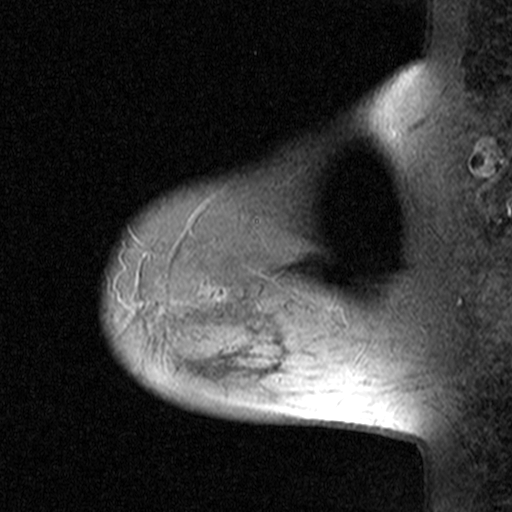
Breast MRI (dynamic contrast-enhanced), one sagittal slice; position 36 of 44 along the scan axis; dynamic contrast-enhanced study with each time point stored as its own series, time point 2 of 3 at this slice position (early post-contrast, ordered by acquisition time); 1.5 T; TE 4.5 ms, TR 11 ms; 512 × 512 image matrix. Patient: female, 38 years. Case-level facts recorded for this patient, not image findings: setting: breast cancer imaged before/during neoadjuvant chemotherapy; receptor status: HR-positive, HER2-negative.
Structures marked on this image (semi-automatically segmented with operator editing):
- analysis volume of interest (the breast-tissue region the enhancement analysis was run in; not a lesion): bounding box [x1, y1, x2, y2] px = [152, 236, 253, 335]
- tumour enhancement mask (voxels above the 90 % enhancement threshold inside the analysis volume of interest): [216, 288, 227, 300]